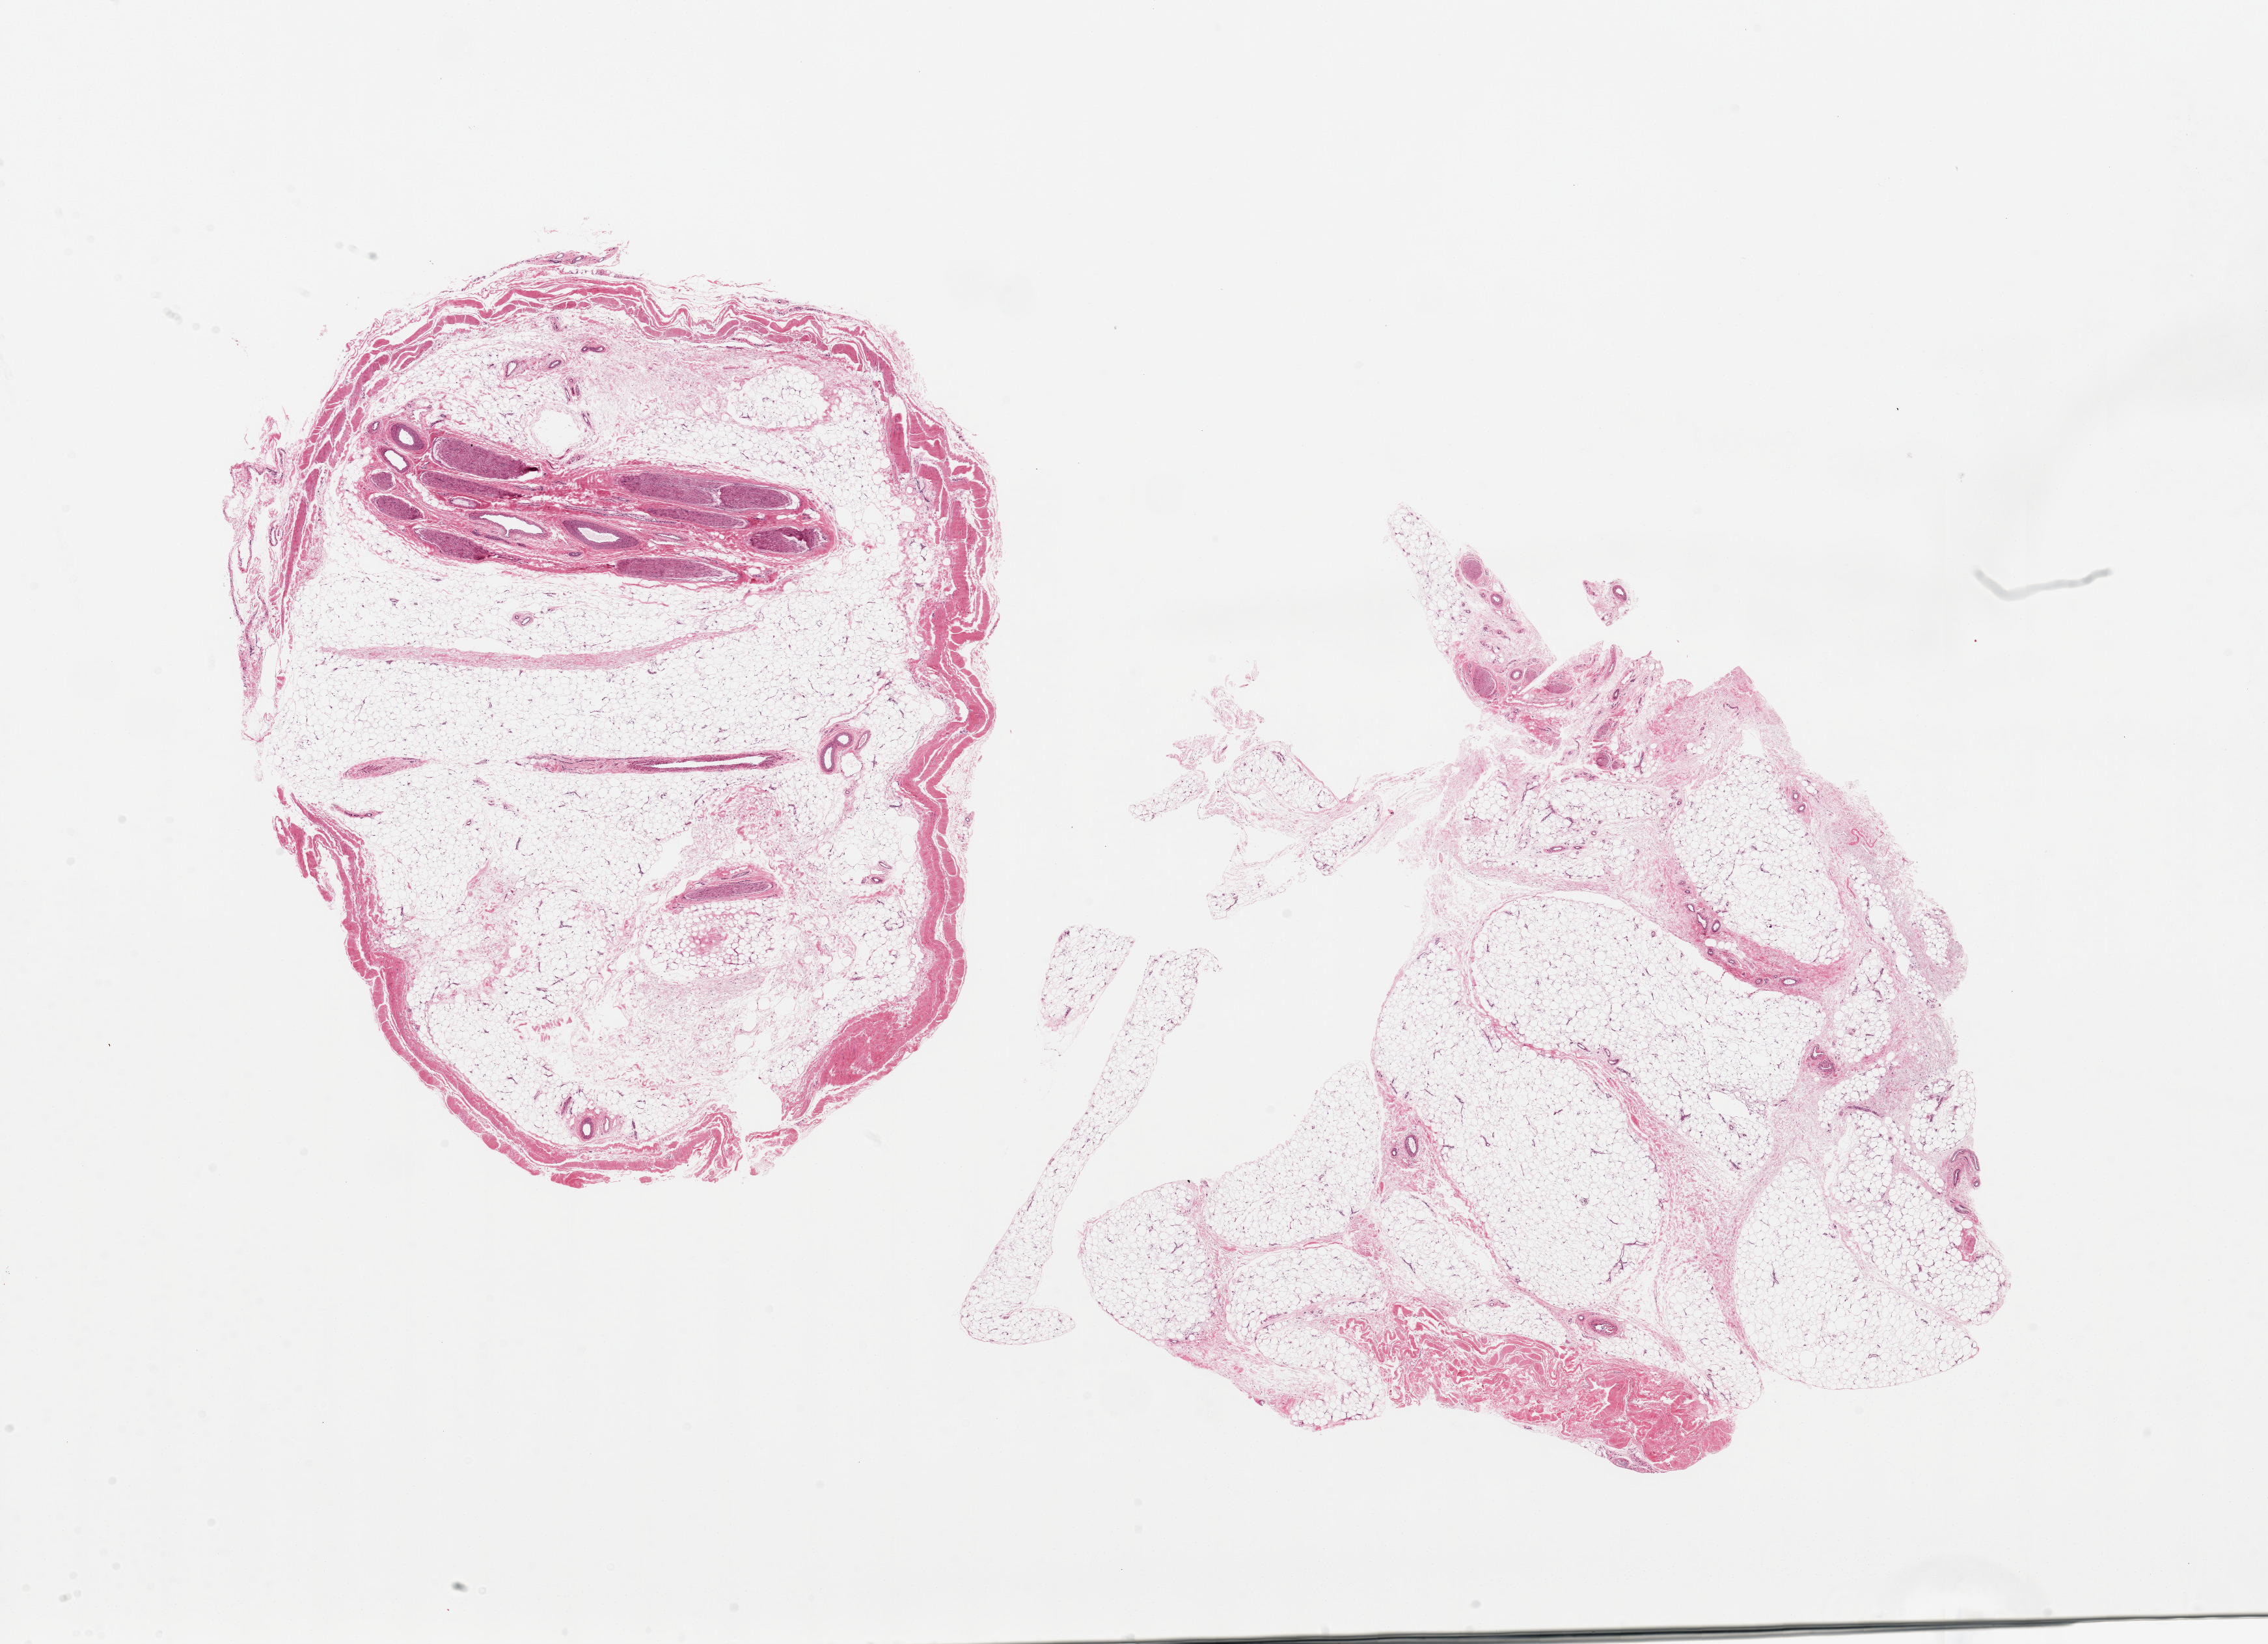
Hematoxylin and eosin (H&E) whole-slide image, brightfield — a low-resolution overview of the entire scanned area, about 27.6 x 20.0 mm; PAXgene-fixed, paraffin-embedded tissue; sampled site (target tissue): adipose tissue; donor tissue sample.
- review note (as recorded): 2 pieces, 12x11 & 11x8mm; 1 has ~15% nerve and blood vessels